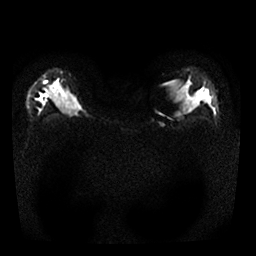
Breast MRI, one axial slice. Slice 17 of 25 in the series (ordered by position). Diffusion-weighted series; image 2 of 4 stored at this slice position (different b-values; order by instance number). 1.5 T. 256 × 256 image matrix. Female patient.
Outlined on this slice (manually delineated by an expert):
- tumour on diffusion-weighted imaging: bounding box <44,81,47,83> (left, top, right, bottom; pixels)